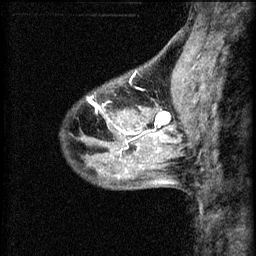
Breast MRI (dynamic contrast-enhanced), one sagittal slice. 3 images stored at this slice position (order not interpretable as contrast timing). 1.5 T. TE 4.2 ms, TR 8.2 ms. 2.2 mm slice thickness. 256 × 256 image matrix, field of view 180 × 180 mm. Female patient, age 40 years.
Outlined on this slice (semi-automatically segmented with operator editing):
- analysis volume of interest (the breast-tissue region the enhancement analysis was run in; not a lesion): bounding box [x1, y1, x2, y2] px = [108, 82, 175, 139]
- tumour enhancement mask (voxels above the 70 % enhancement threshold inside the analysis volume of interest): [112, 112, 171, 137]